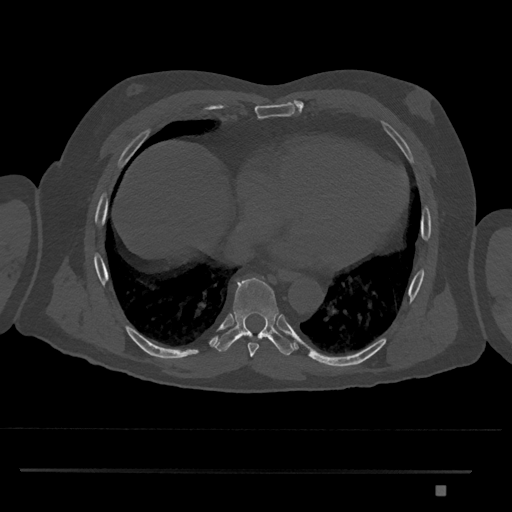
CT including the spine, one axial slice; slice 1127 of 1134 in the series (ordered by position); reconstruction kernel Br40s/3; bone window (W 1800 / L 400 HU); 512 × 512 image matrix, field of view 429 × 429 mm. Patient: male, 65 years. From the clinical record (not read from this slice): primary cancer: prostate.
Outlined on this slice (semi-automatically segmented with operator editing):
- T8 vertebra: bounding box [x1, y1, x2, y2] px = [215, 277, 296, 357]